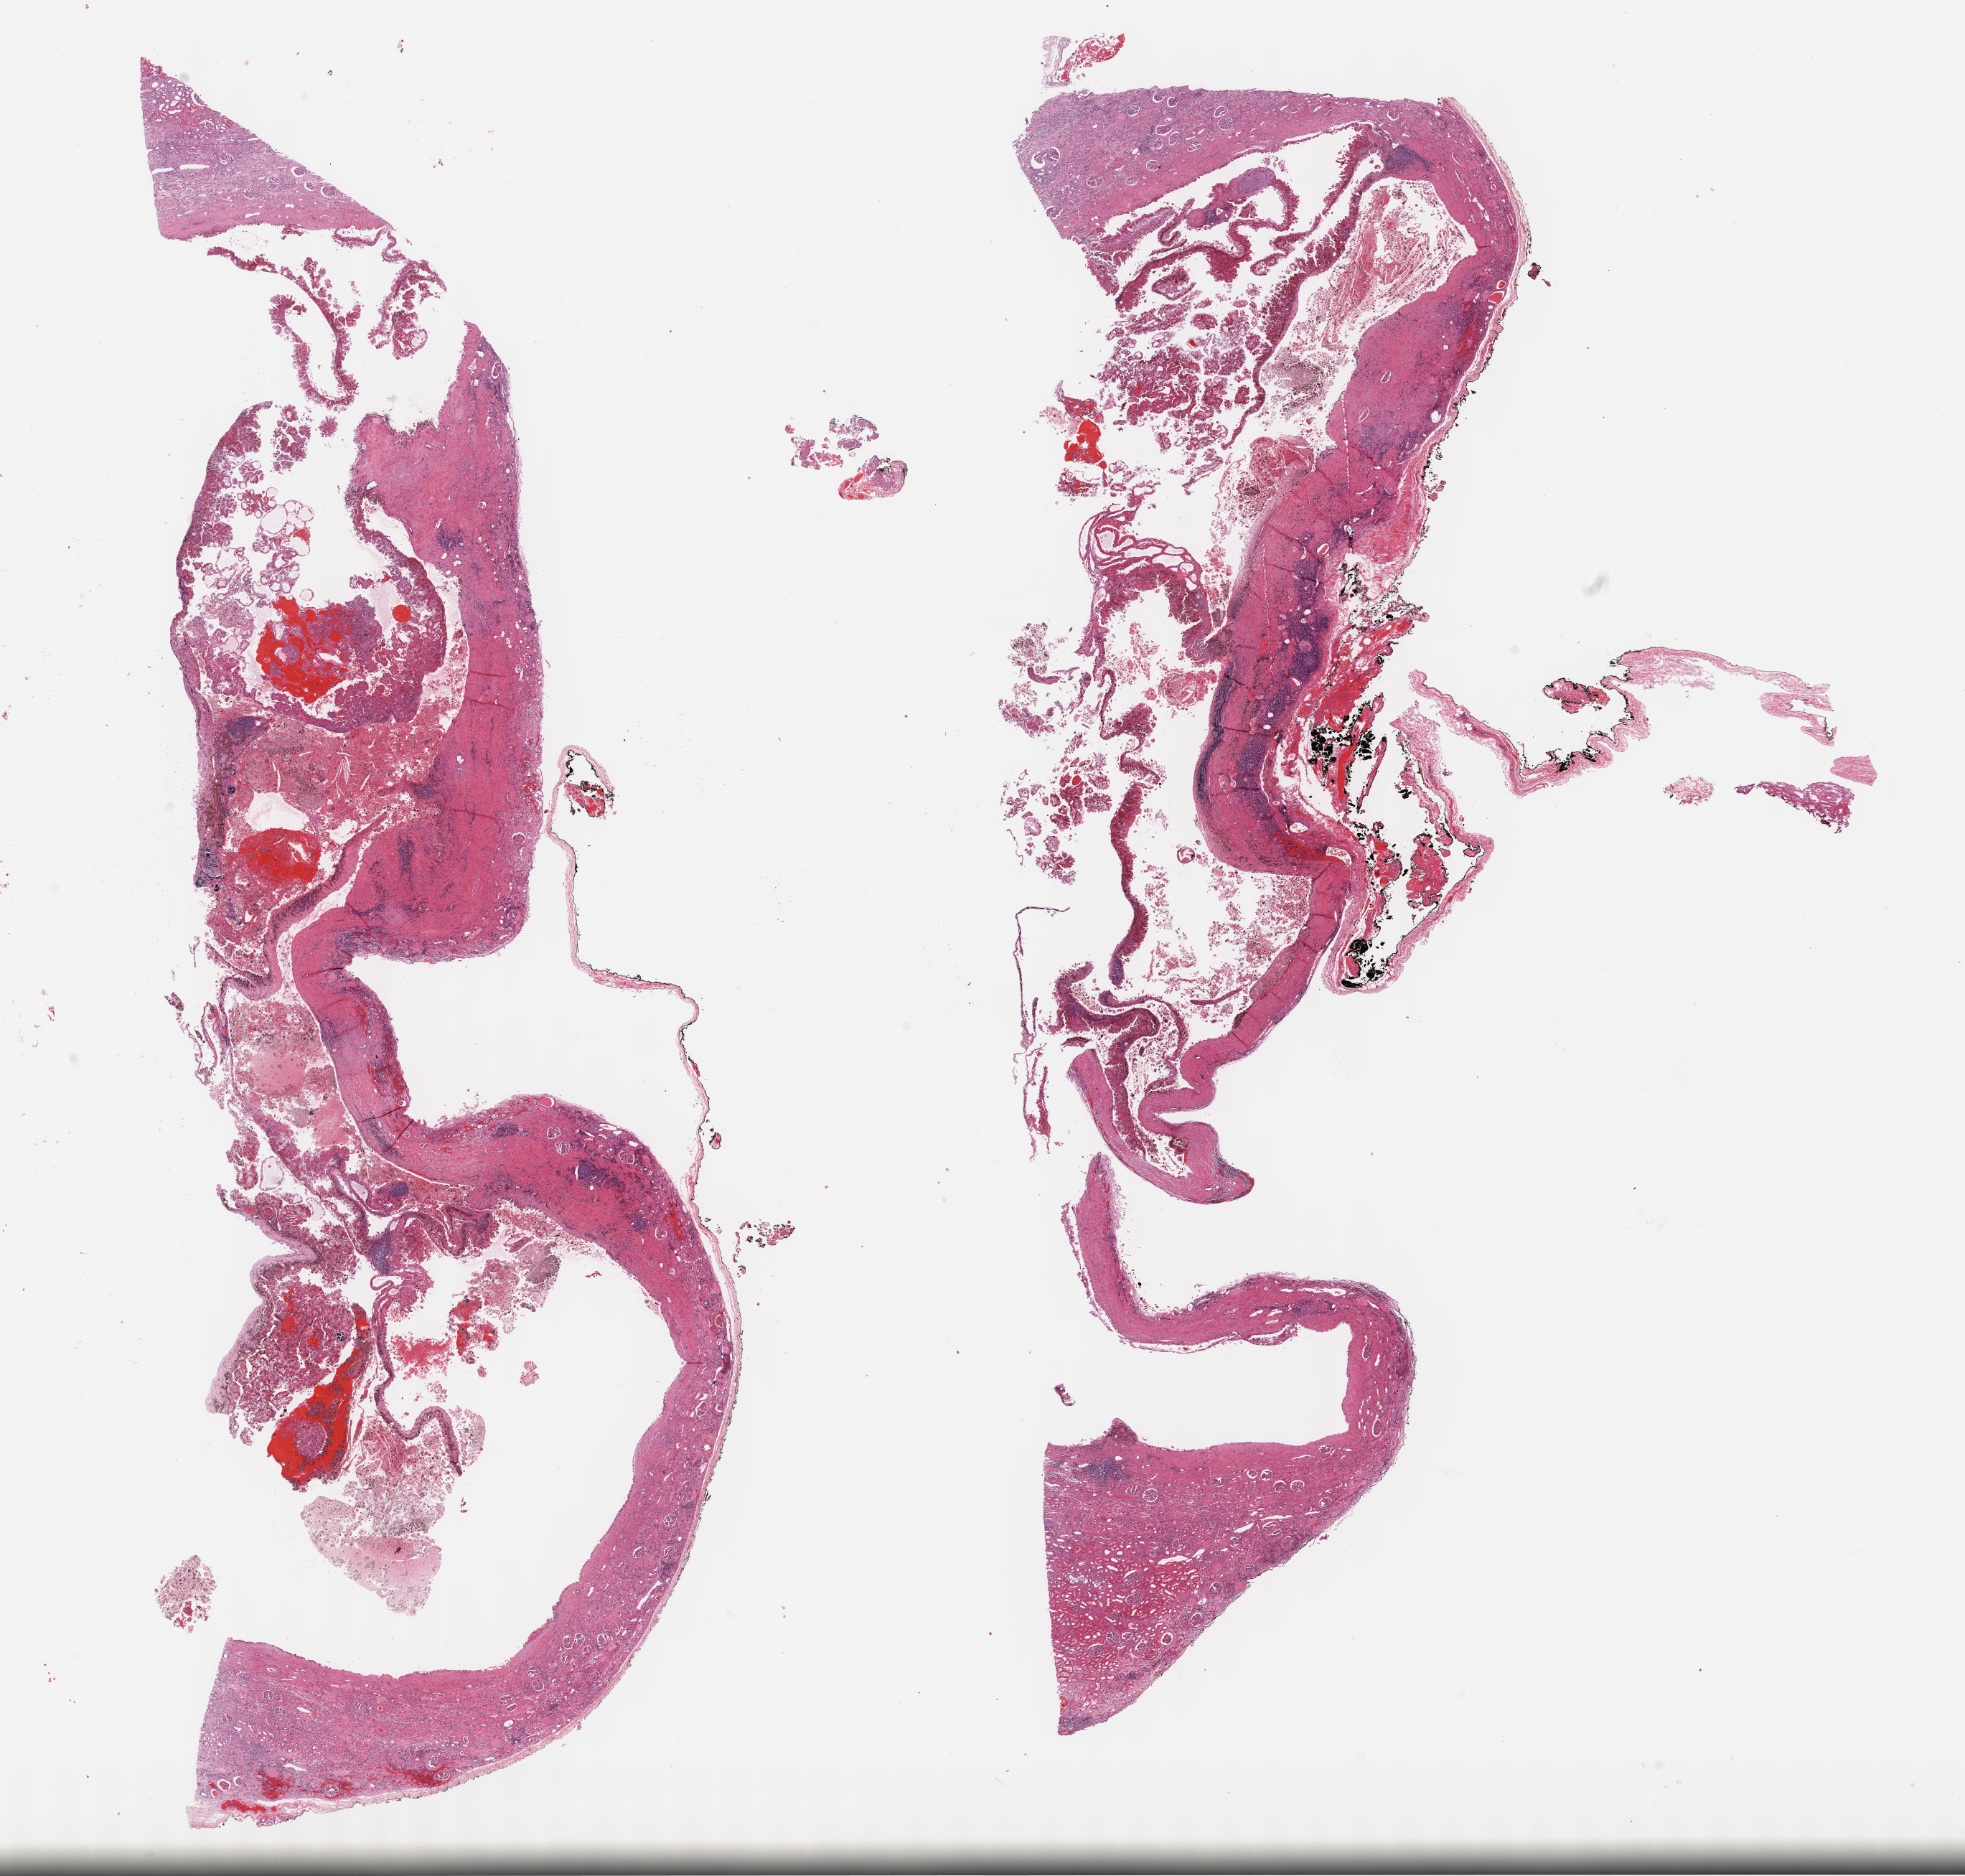
Digitized Hematoxylin and eosin (H&E) stained tissue section (whole slide), a low-resolution overview of the entire scanned area, about 22.1 x 21.1 mm, formalin-fixed paraffin-embedded (FFPE) diagnostic section, primary tumour sample from the kidney. Male, age 61 years at initial diagnosis.
Pathologic diagnosis: Papillary adenocarcinoma, NOS. Laterality: left. AJCC pathologic stage: I (7th edition).